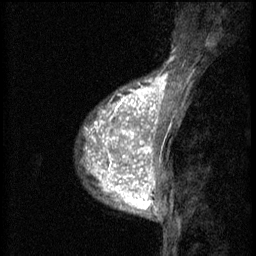
Breast MRI (dynamic contrast-enhanced), one sagittal slice. Slice 17 of 60 in the series (ordered by position). 3 images stored at this slice position (order not interpretable as contrast timing). 1.5 T. TE 4.2 ms, TR 8.2 ms. 2 mm slice thickness. 256 × 256 image matrix, field of view 180 × 180 mm. Patient: female, 38 years.
Annotated regions visible in this slice (semi-automatic segmentation, software-assisted and operator-edited):
- analysis volume of interest (the breast-tissue region the enhancement analysis was run in; not a lesion): bounding box [x1, y1, x2, y2] px = [92, 112, 152, 171]
- tumour enhancement mask (voxels above the 70 % enhancement threshold inside the analysis volume of interest): [92, 112, 152, 171]